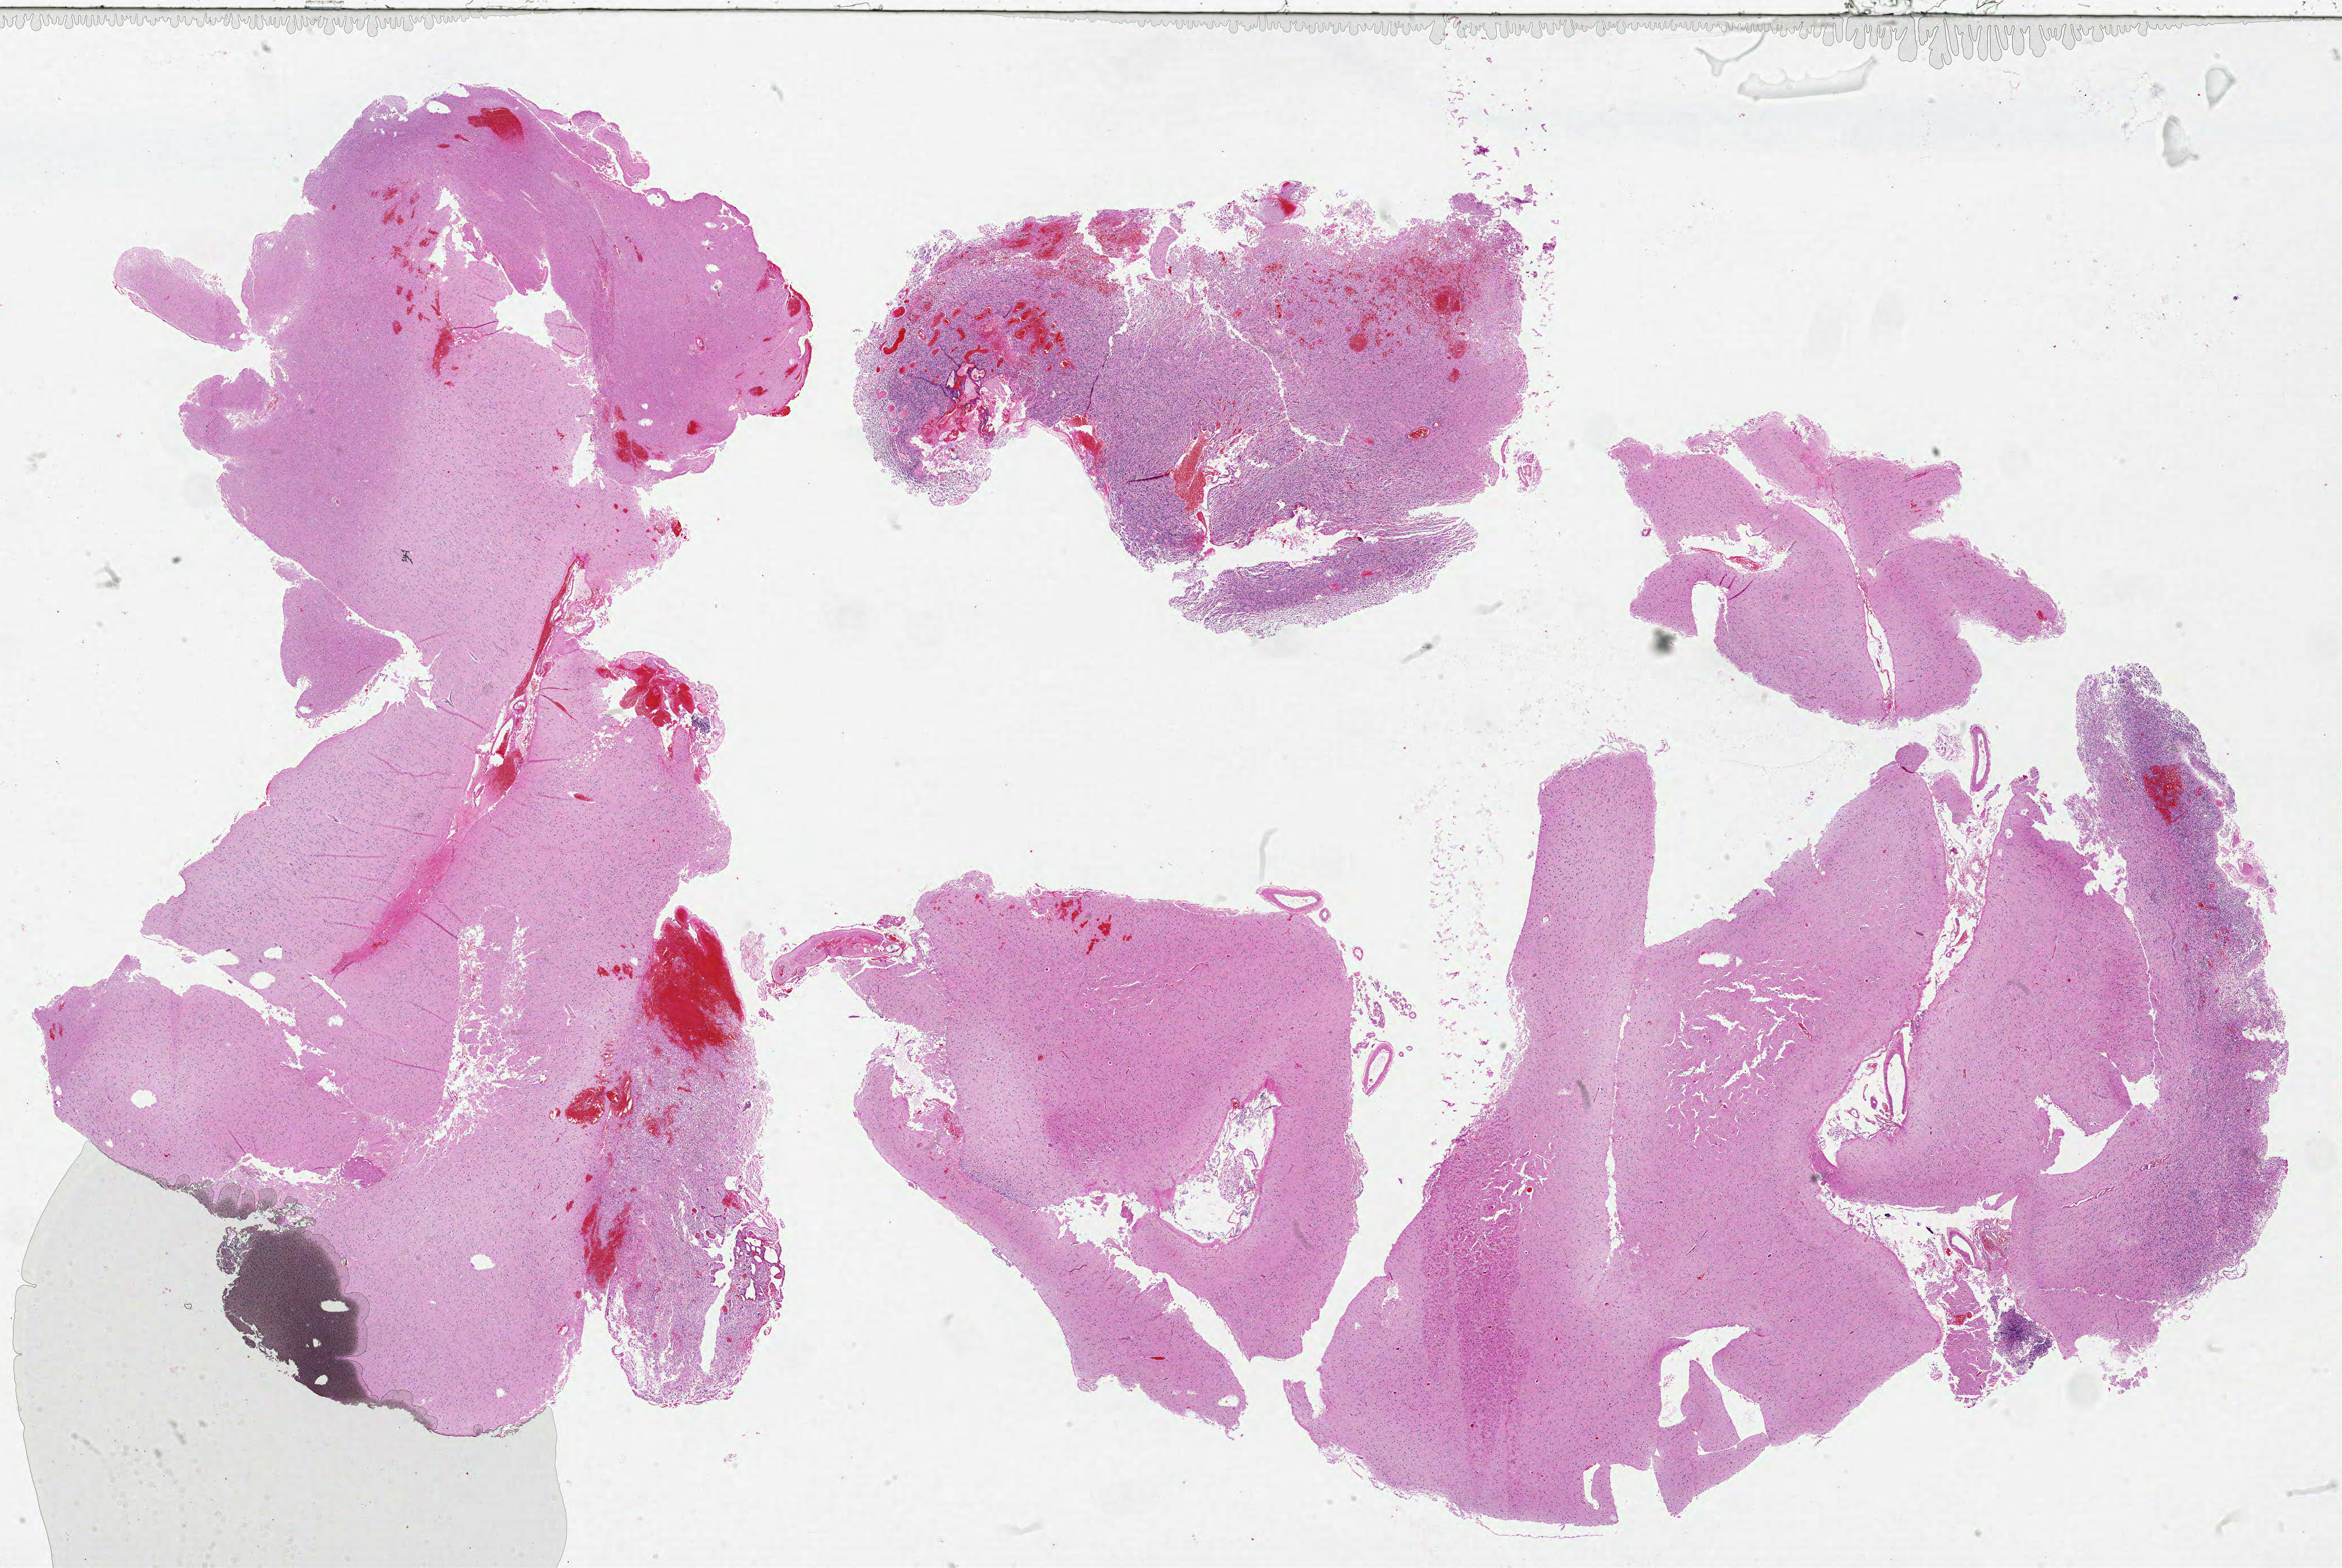
Hematoxylin and eosin (H&E) stained whole-slide image — whole scanned area (about 33.0 x 22.1 mm, slide scanned at 20x) shown as a low-resolution overview; formalin-fixed paraffin-embedded (FFPE) diagnostic section; brain, primary tumour sample. Patient: male, age at initial diagnosis 60 years.
Pathologic diagnosis: Glioblastoma.